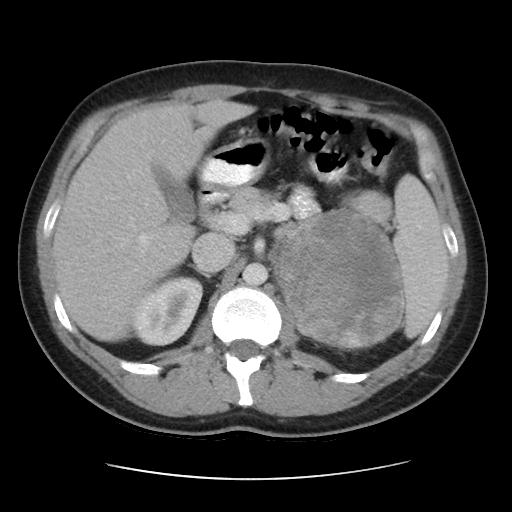
Contrast-enhanced abdominal CT, one axial slice. Slice 27 of 48 in the series (ordered by position). Reconstruction kernel STANDARD. 120 kVp. Intravenous contrast given. Soft-tissue window (W 400 / L 40 HU). 5 mm slice thickness. 512 × 512 image matrix, field of view 360 × 360 mm. Male patient, age 32 years. Case-level facts recorded for this patient, not image findings: diagnosis: adrenocortical carcinoma; tumour side: left adrenal; tumour size at pathology: 14 cm; Ki-67 index: 67 %; stage (as recorded): 3.
Outlined on this slice (semi-automatically segmented with operator editing):
- mass: bounding box (x1, y1, x2, y2) in pixels: (278, 213, 400, 348)